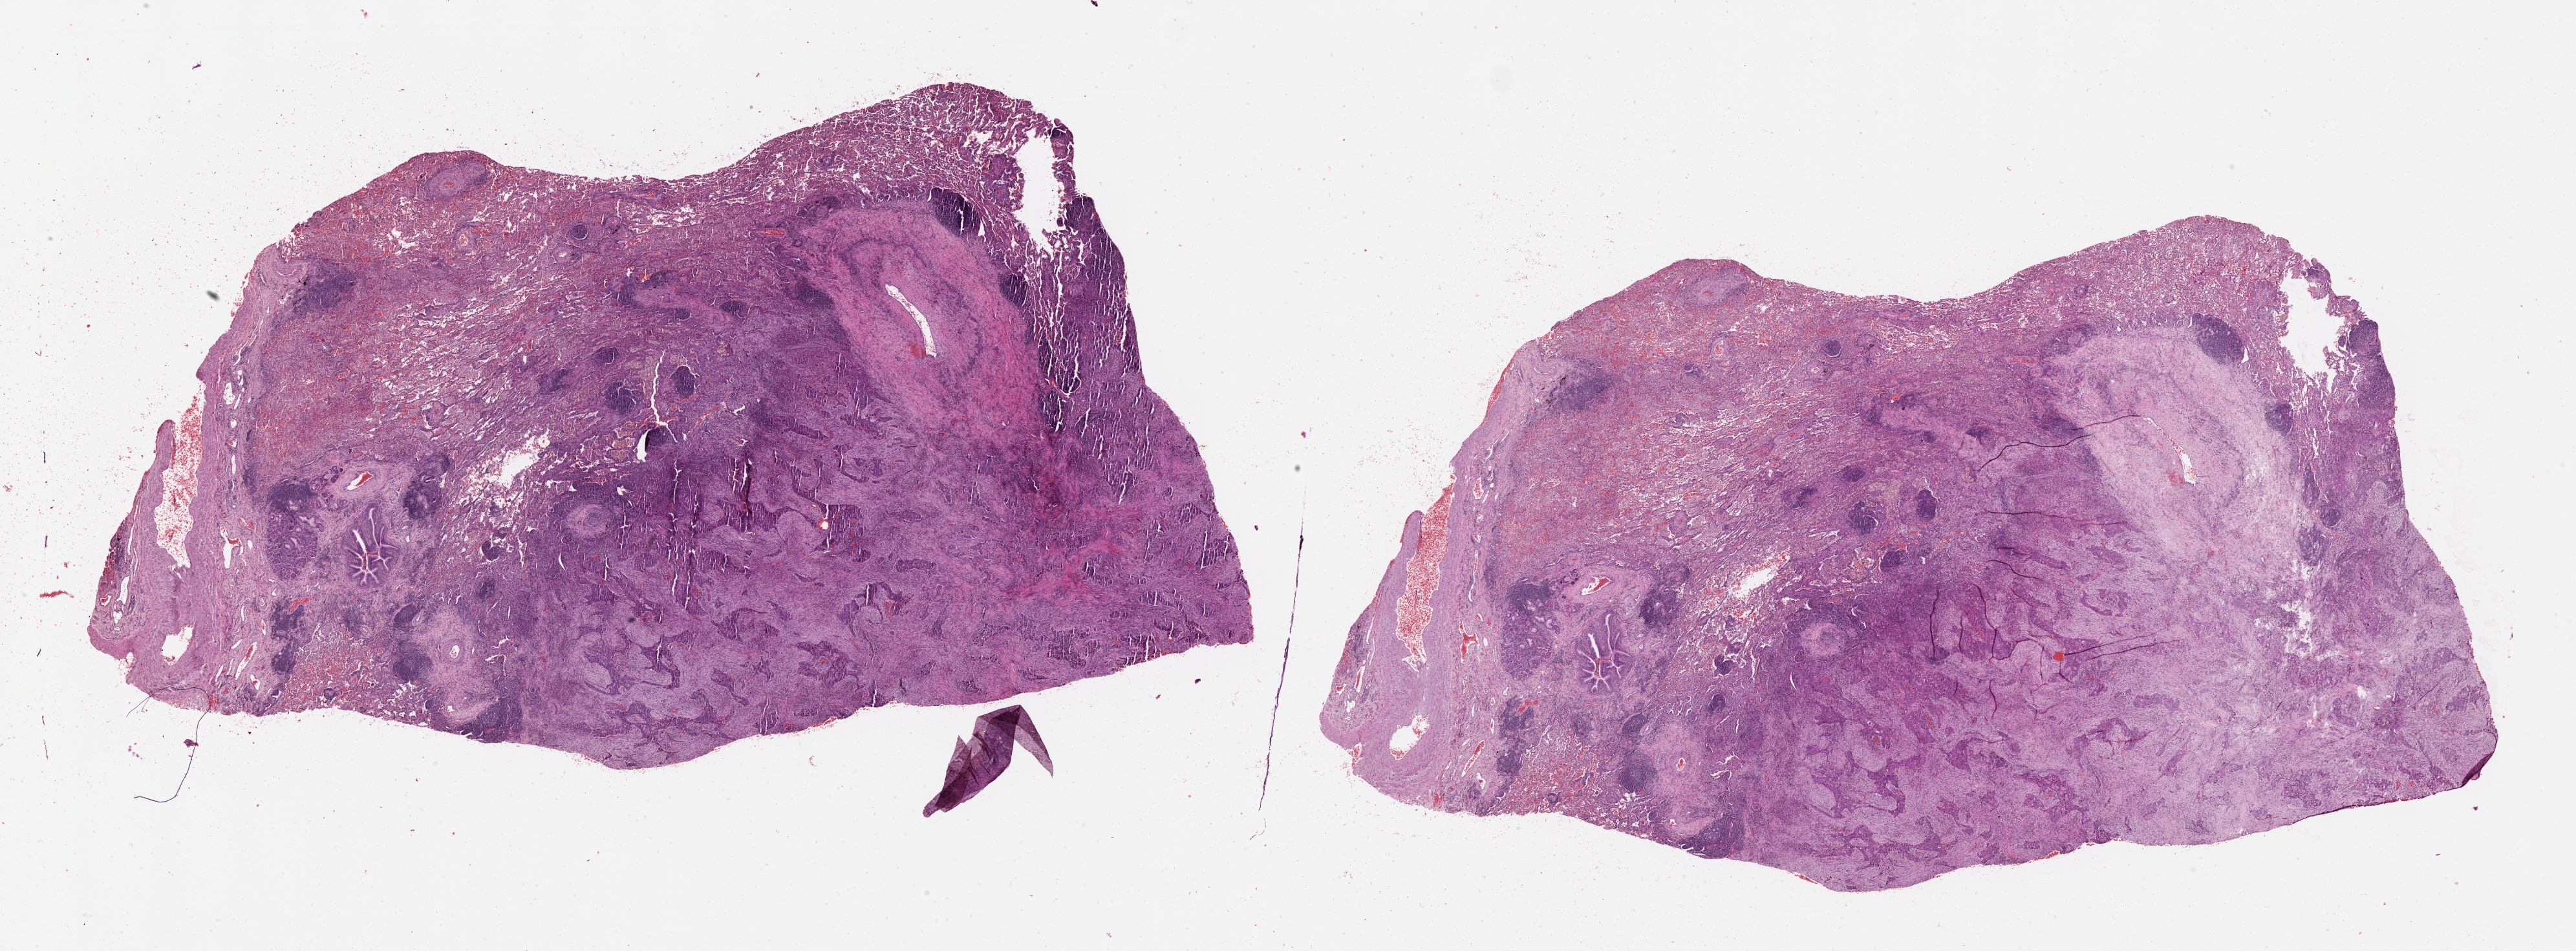
Digitized Hematoxylin and eosin (H&E) stained tissue section (whole slide) — low-resolution overview of the scanned area, about 32.1 x 11.8 mm; tumour tissue sample, lung. Female, 62 y/o.
Patient diagnosis (cohort enrolment): squamous cell carcinoma (lung).